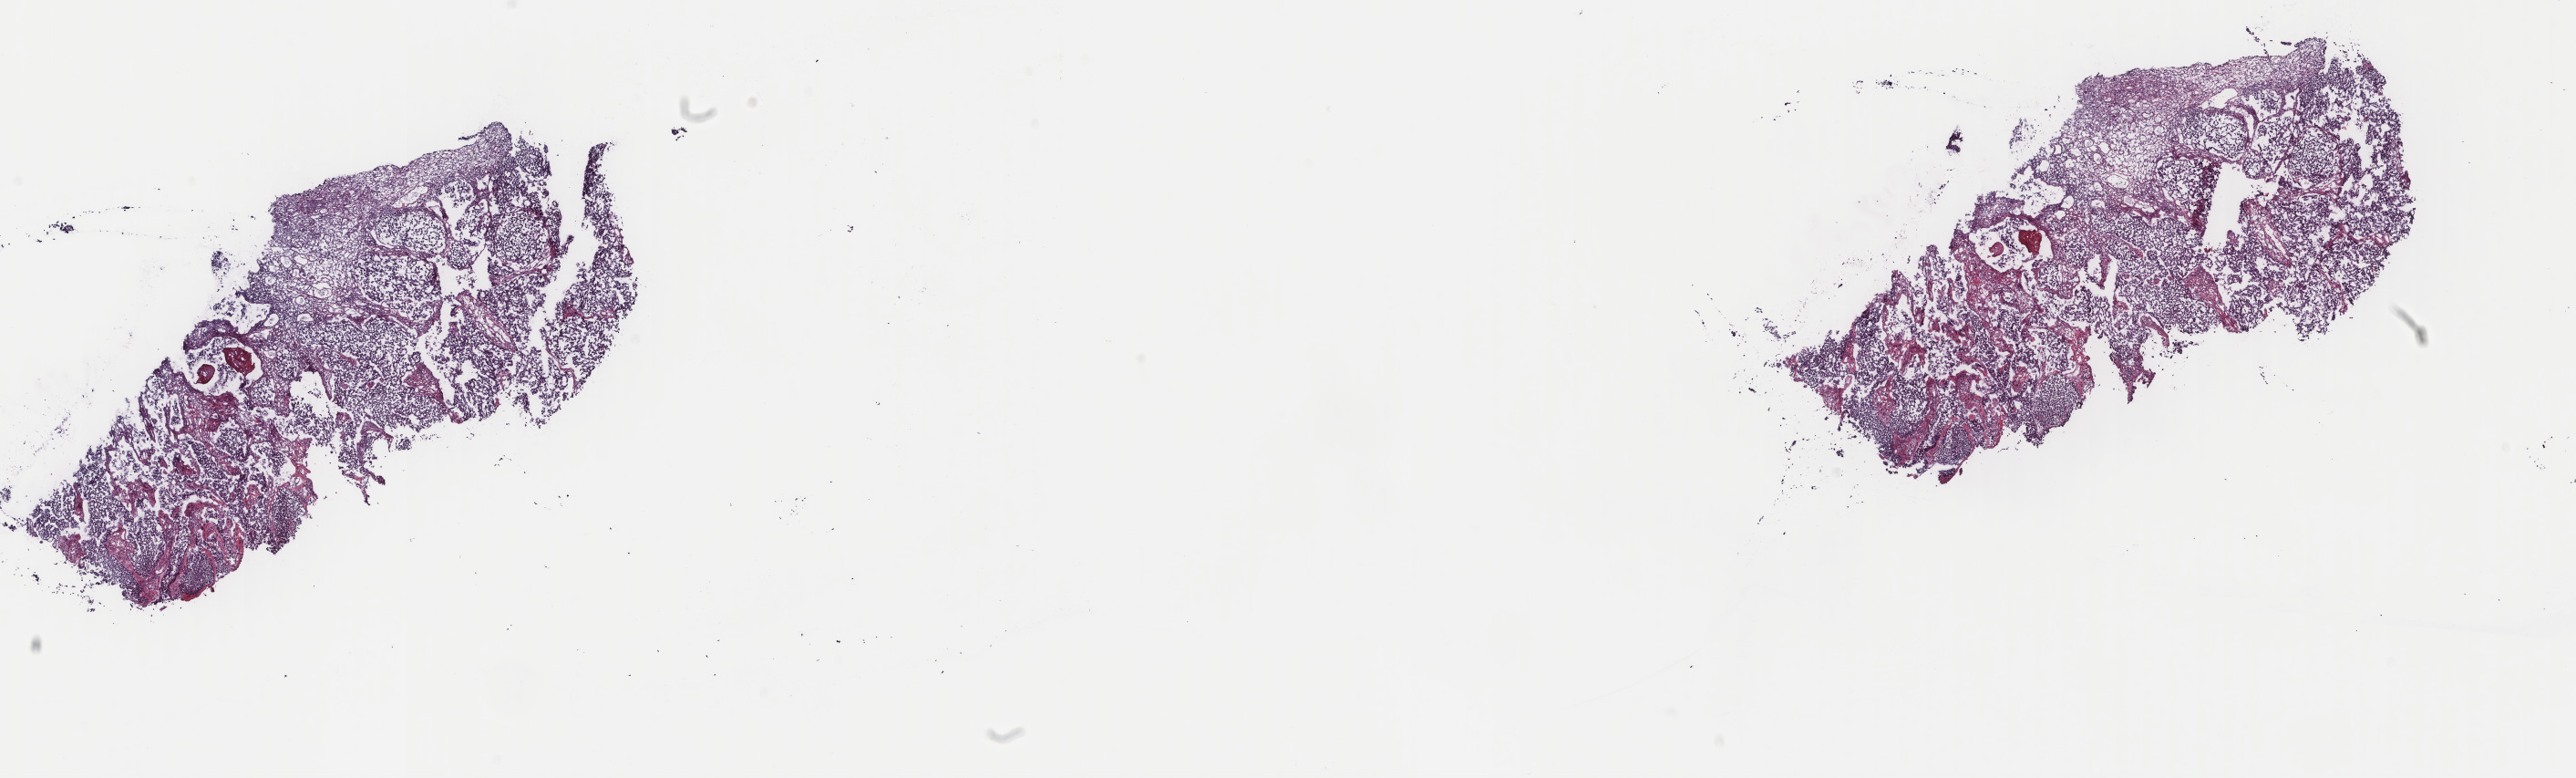
H&E whole-slide image, low-resolution overview of the scanned area, about 22.4 x 6.8 mm (acquisition: 40x scan). Frozen section from the top of the tissue portion. Sample: primary tumour, bladder. Female patient; age at initial diagnosis 82 years. Histologic grade: high grade. Slide review estimates, as recorded: tumour cells 66%, tumour nuclei 85%, normal cells 0%, stromal cells 30%, necrosis 4%. Inflammatory infiltration, as recorded: lymphocyte infiltration 10%, monocyte infiltration 0%, neutrophil infiltration 1%.
AJCC pathologic stage: II. Histologic diagnosis: Transitional cell carcinoma (dome of bladder).